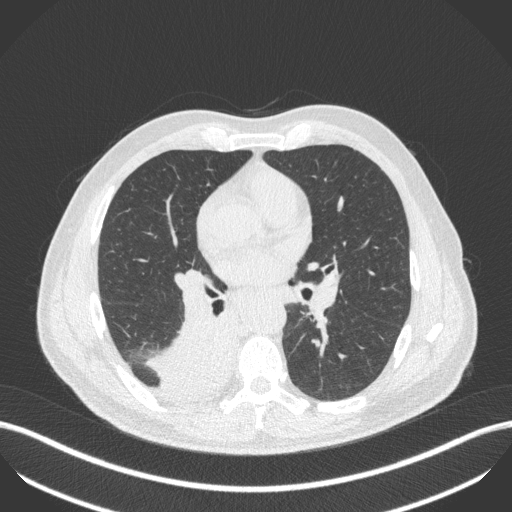
Chest CT, one axial slice; slice 251 of 451 in the series (ordered by position); reconstruction kernel B31f; 100 kVp; lung window (W 1500 / L -600 HU); 1 mm slice thickness; 512 × 512 image matrix, field of view 400 × 400 mm. Male patient, age 61 years. From the clinical record (not read from this slice): clinical TNM (as recorded): T1 N0 M0.
Structures marked on this image (bounding box drawn by a radiologist):
- lung tumour (recorded histology: small cell carcinoma): bounding box (x1, y1, x2, y2) in pixels: (146, 311, 231, 403)